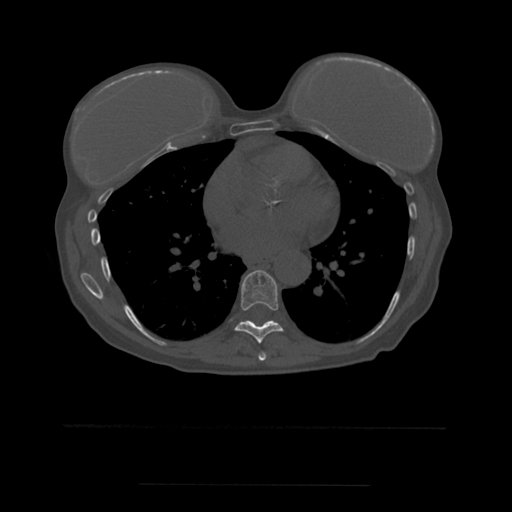
CT including the spine, one axial slice. Position 338 of 544 along the scan axis. Bone window (W 1800 / L 400 HU). 512 × 512 image matrix. Patient age 58 years. From the clinical record (not read from this slice): primary cancer: lung.
Annotated regions visible in this slice (semi-automatically segmented with operator editing):
- T7 vertebra: bounding box [x1, y1, x2, y2] px = [258, 352, 267, 361]
- T8 vertebra: [235, 270, 284, 344]